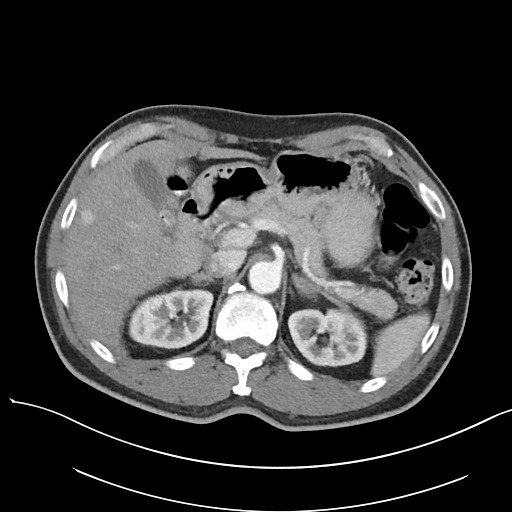
Contrast-enhanced abdominal CT, one axial slice; reconstruction kernel I30f/3; 120 kVp; intravenous contrast given; soft-tissue window (W 400 / L 40 HU); 5 mm slice thickness; 512 × 512 image matrix. Patient: male, 63 years. From the clinical record (not read from this slice): diagnosis: adrenocortical carcinoma; tumour side: left adrenal.
Outlined on this slice (semi-automatically segmented with operator editing):
- mass: box from (x=293, y=274) to (x=318, y=296) px